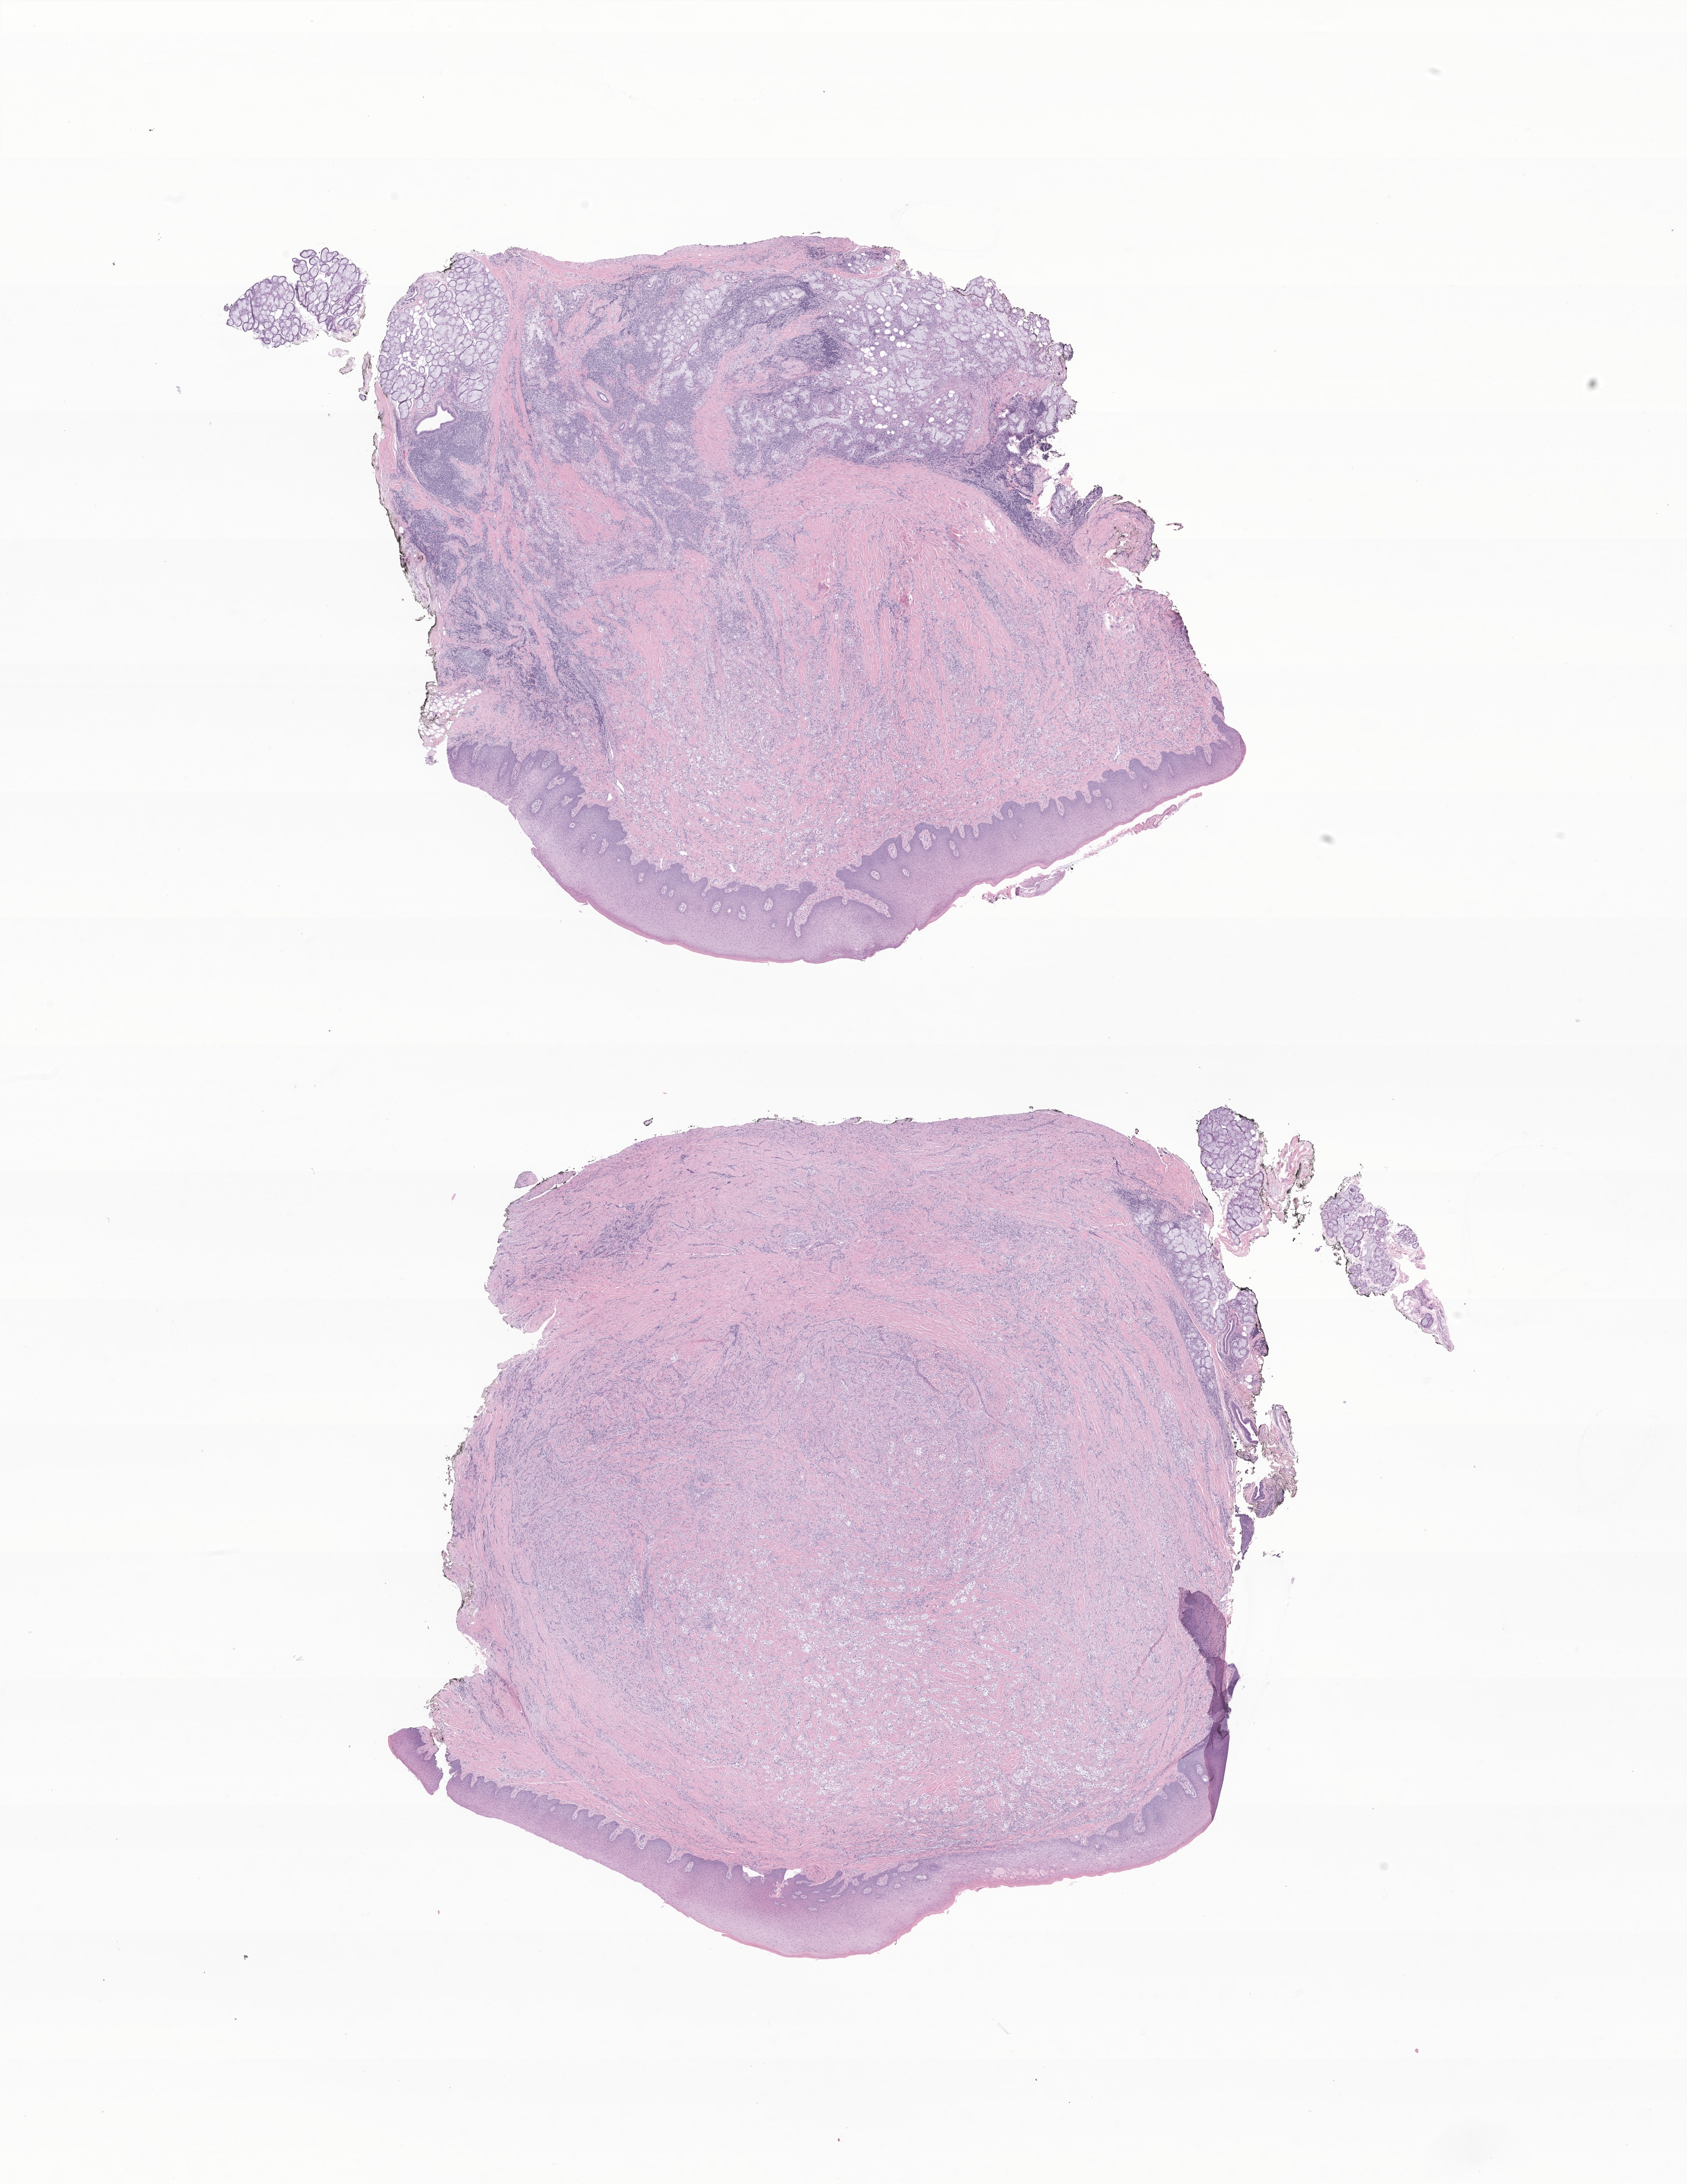
Haematoxylin and eosin whole-slide image of tumor tissue from the hard palate — whole scanned area (about 14.2 x 18.4 mm) shown as a low-resolution overview; FFPE section. Male patient, age 137 months (11 years 5 months).
* diagnosis: Carcinoma, NOS